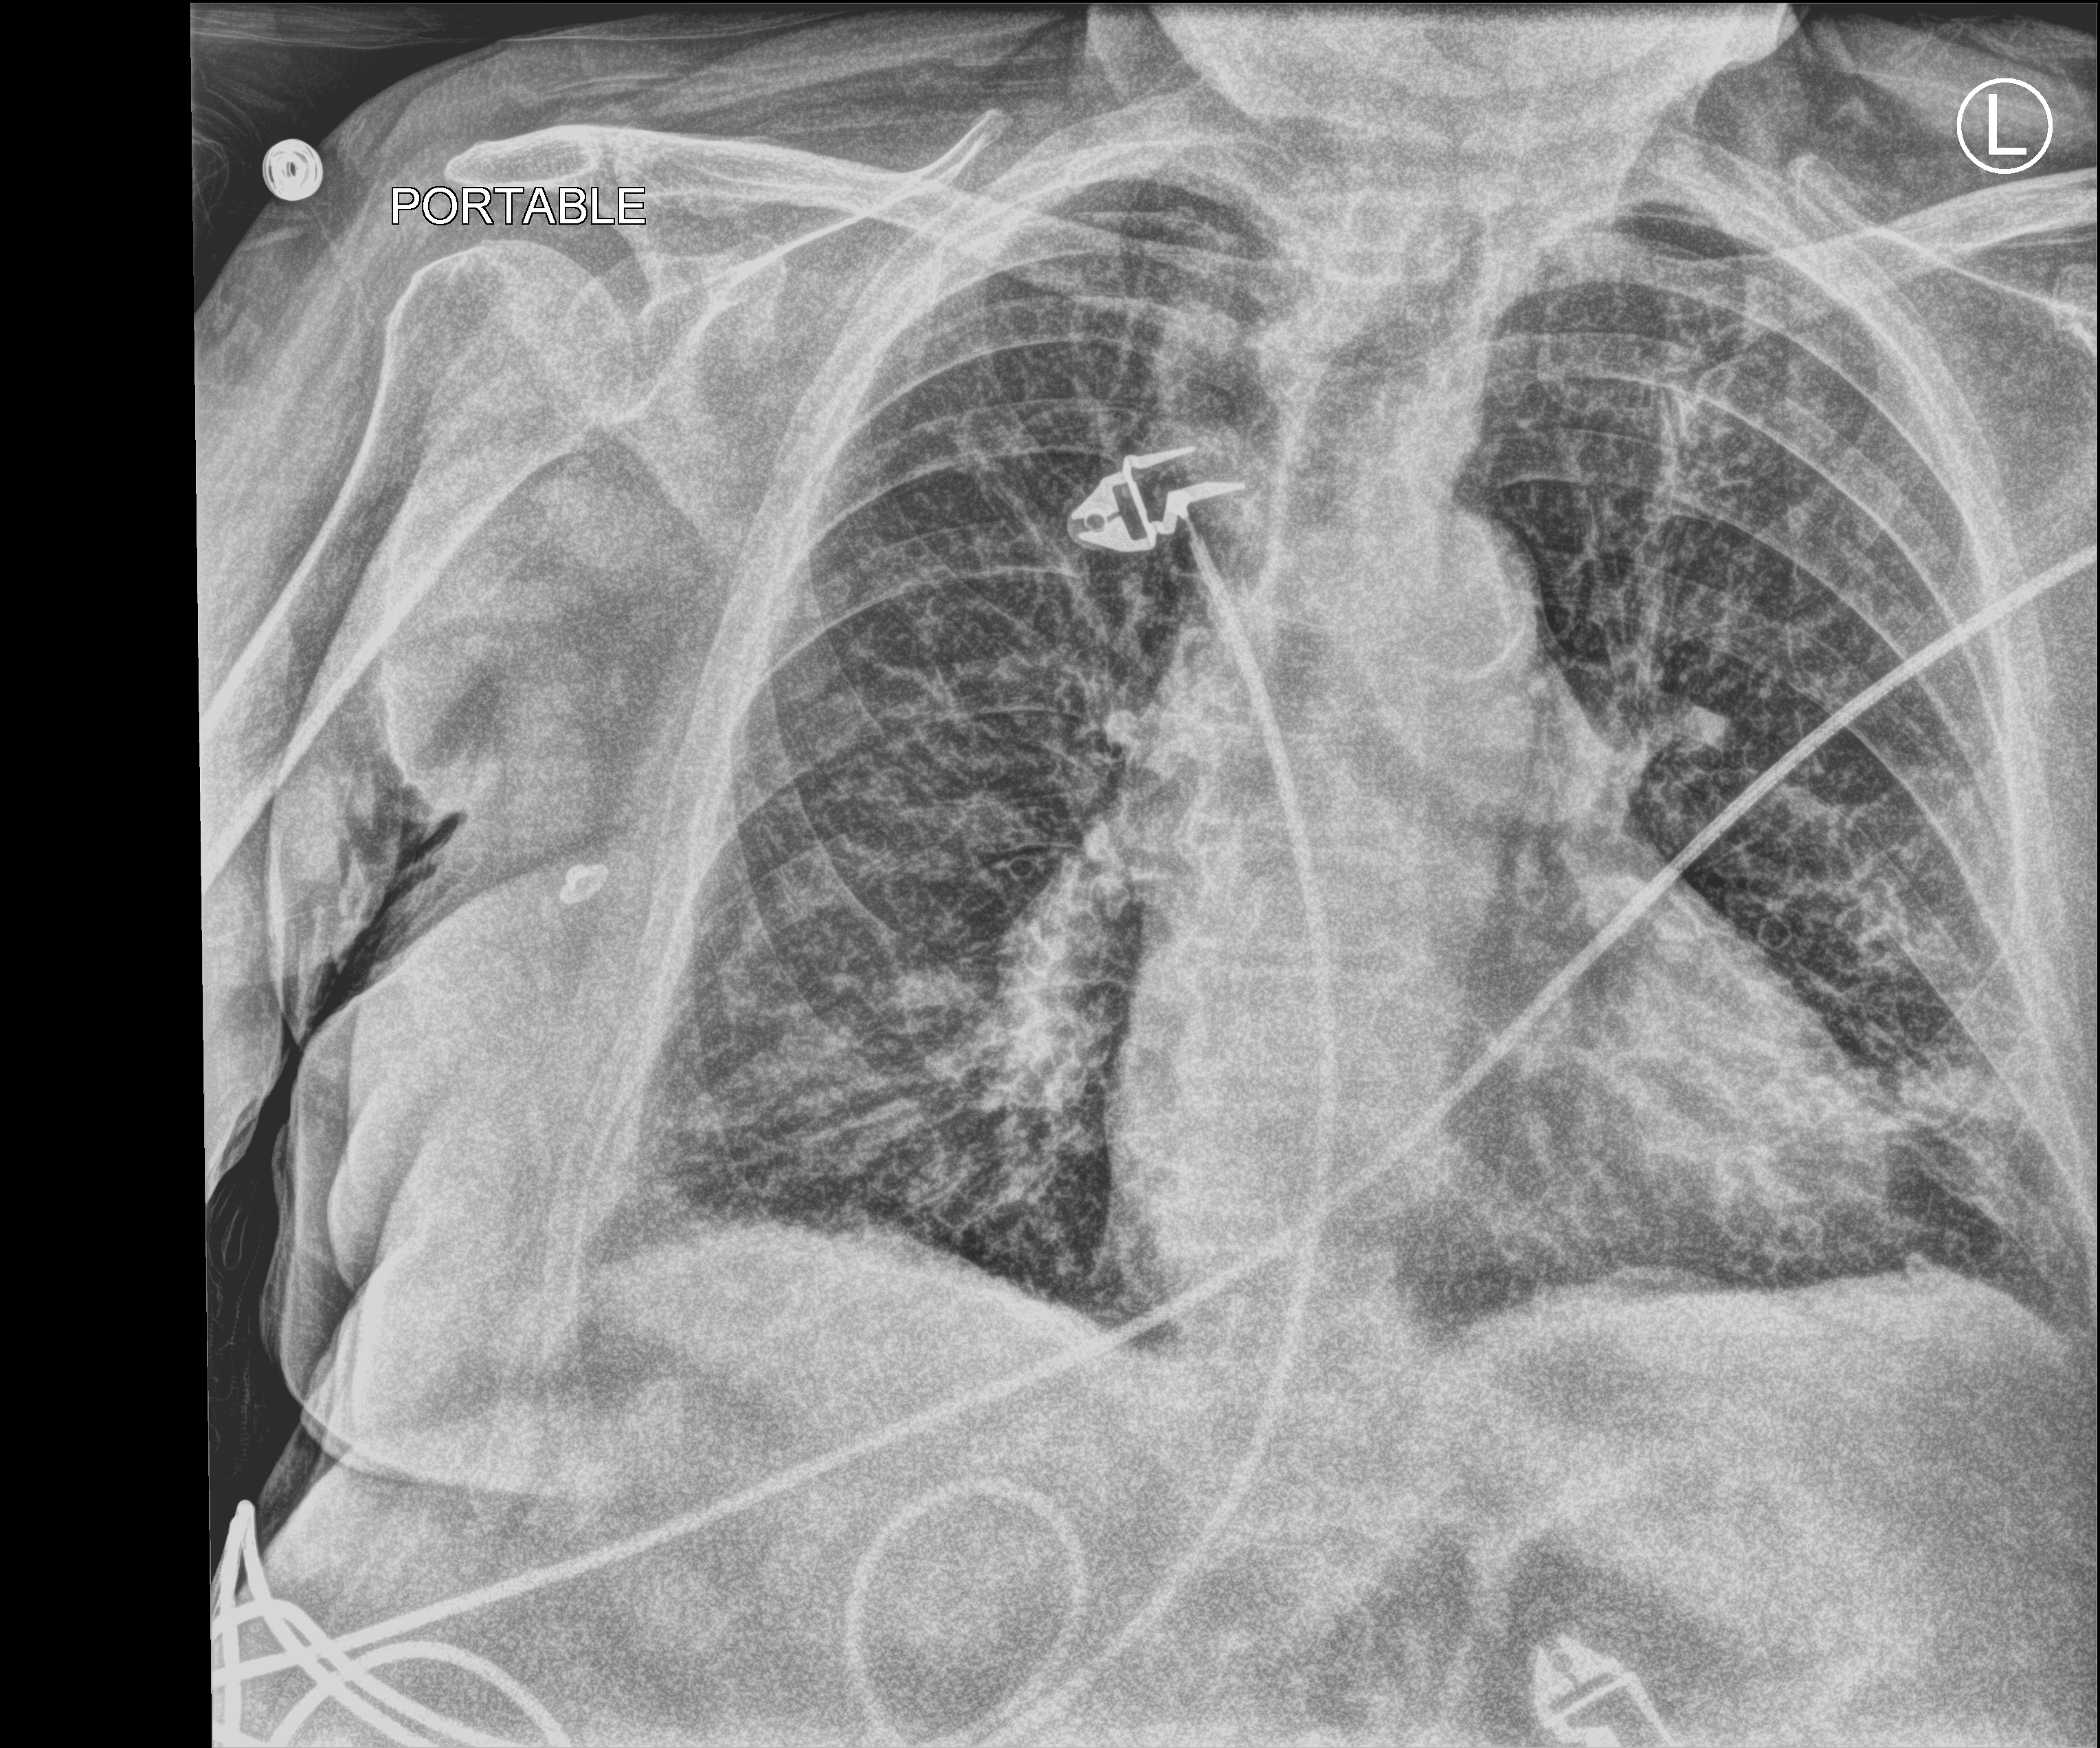
Portable chest radiograph. Patient hospitalised with COVID-19; female, aged 75–90 years.
Admission-level facts for this patient (not findings on this image; timing relative to this image not recorded):
- hypertension (admission record): no
- admitted to intensive care during this hospital stay: no